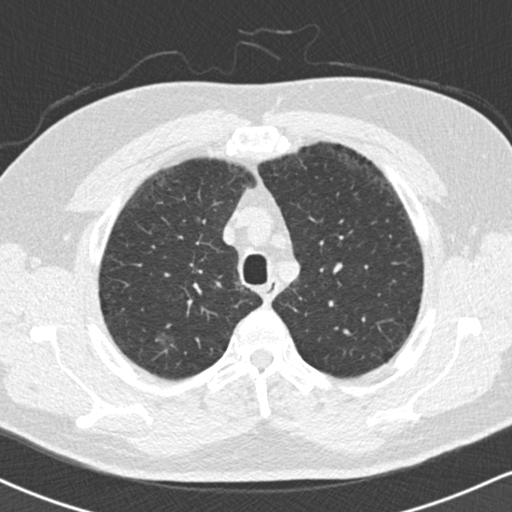
Low-dose screening chest CT, one axial slice. Slice 133 of 169 in the series (ordered by position). Reconstruction kernel B30f. 120 kVp. Lung window (W 1500 / L -600 HU). 2 mm slice thickness. 512 × 512 image matrix, field of view 320 × 320 mm.
Outlined on this slice (manually delineated by an expert):
- lesion 1 (tumor, upper lobe of right lung): bounding box <156,331,175,347> (left, top, right, bottom; pixels)